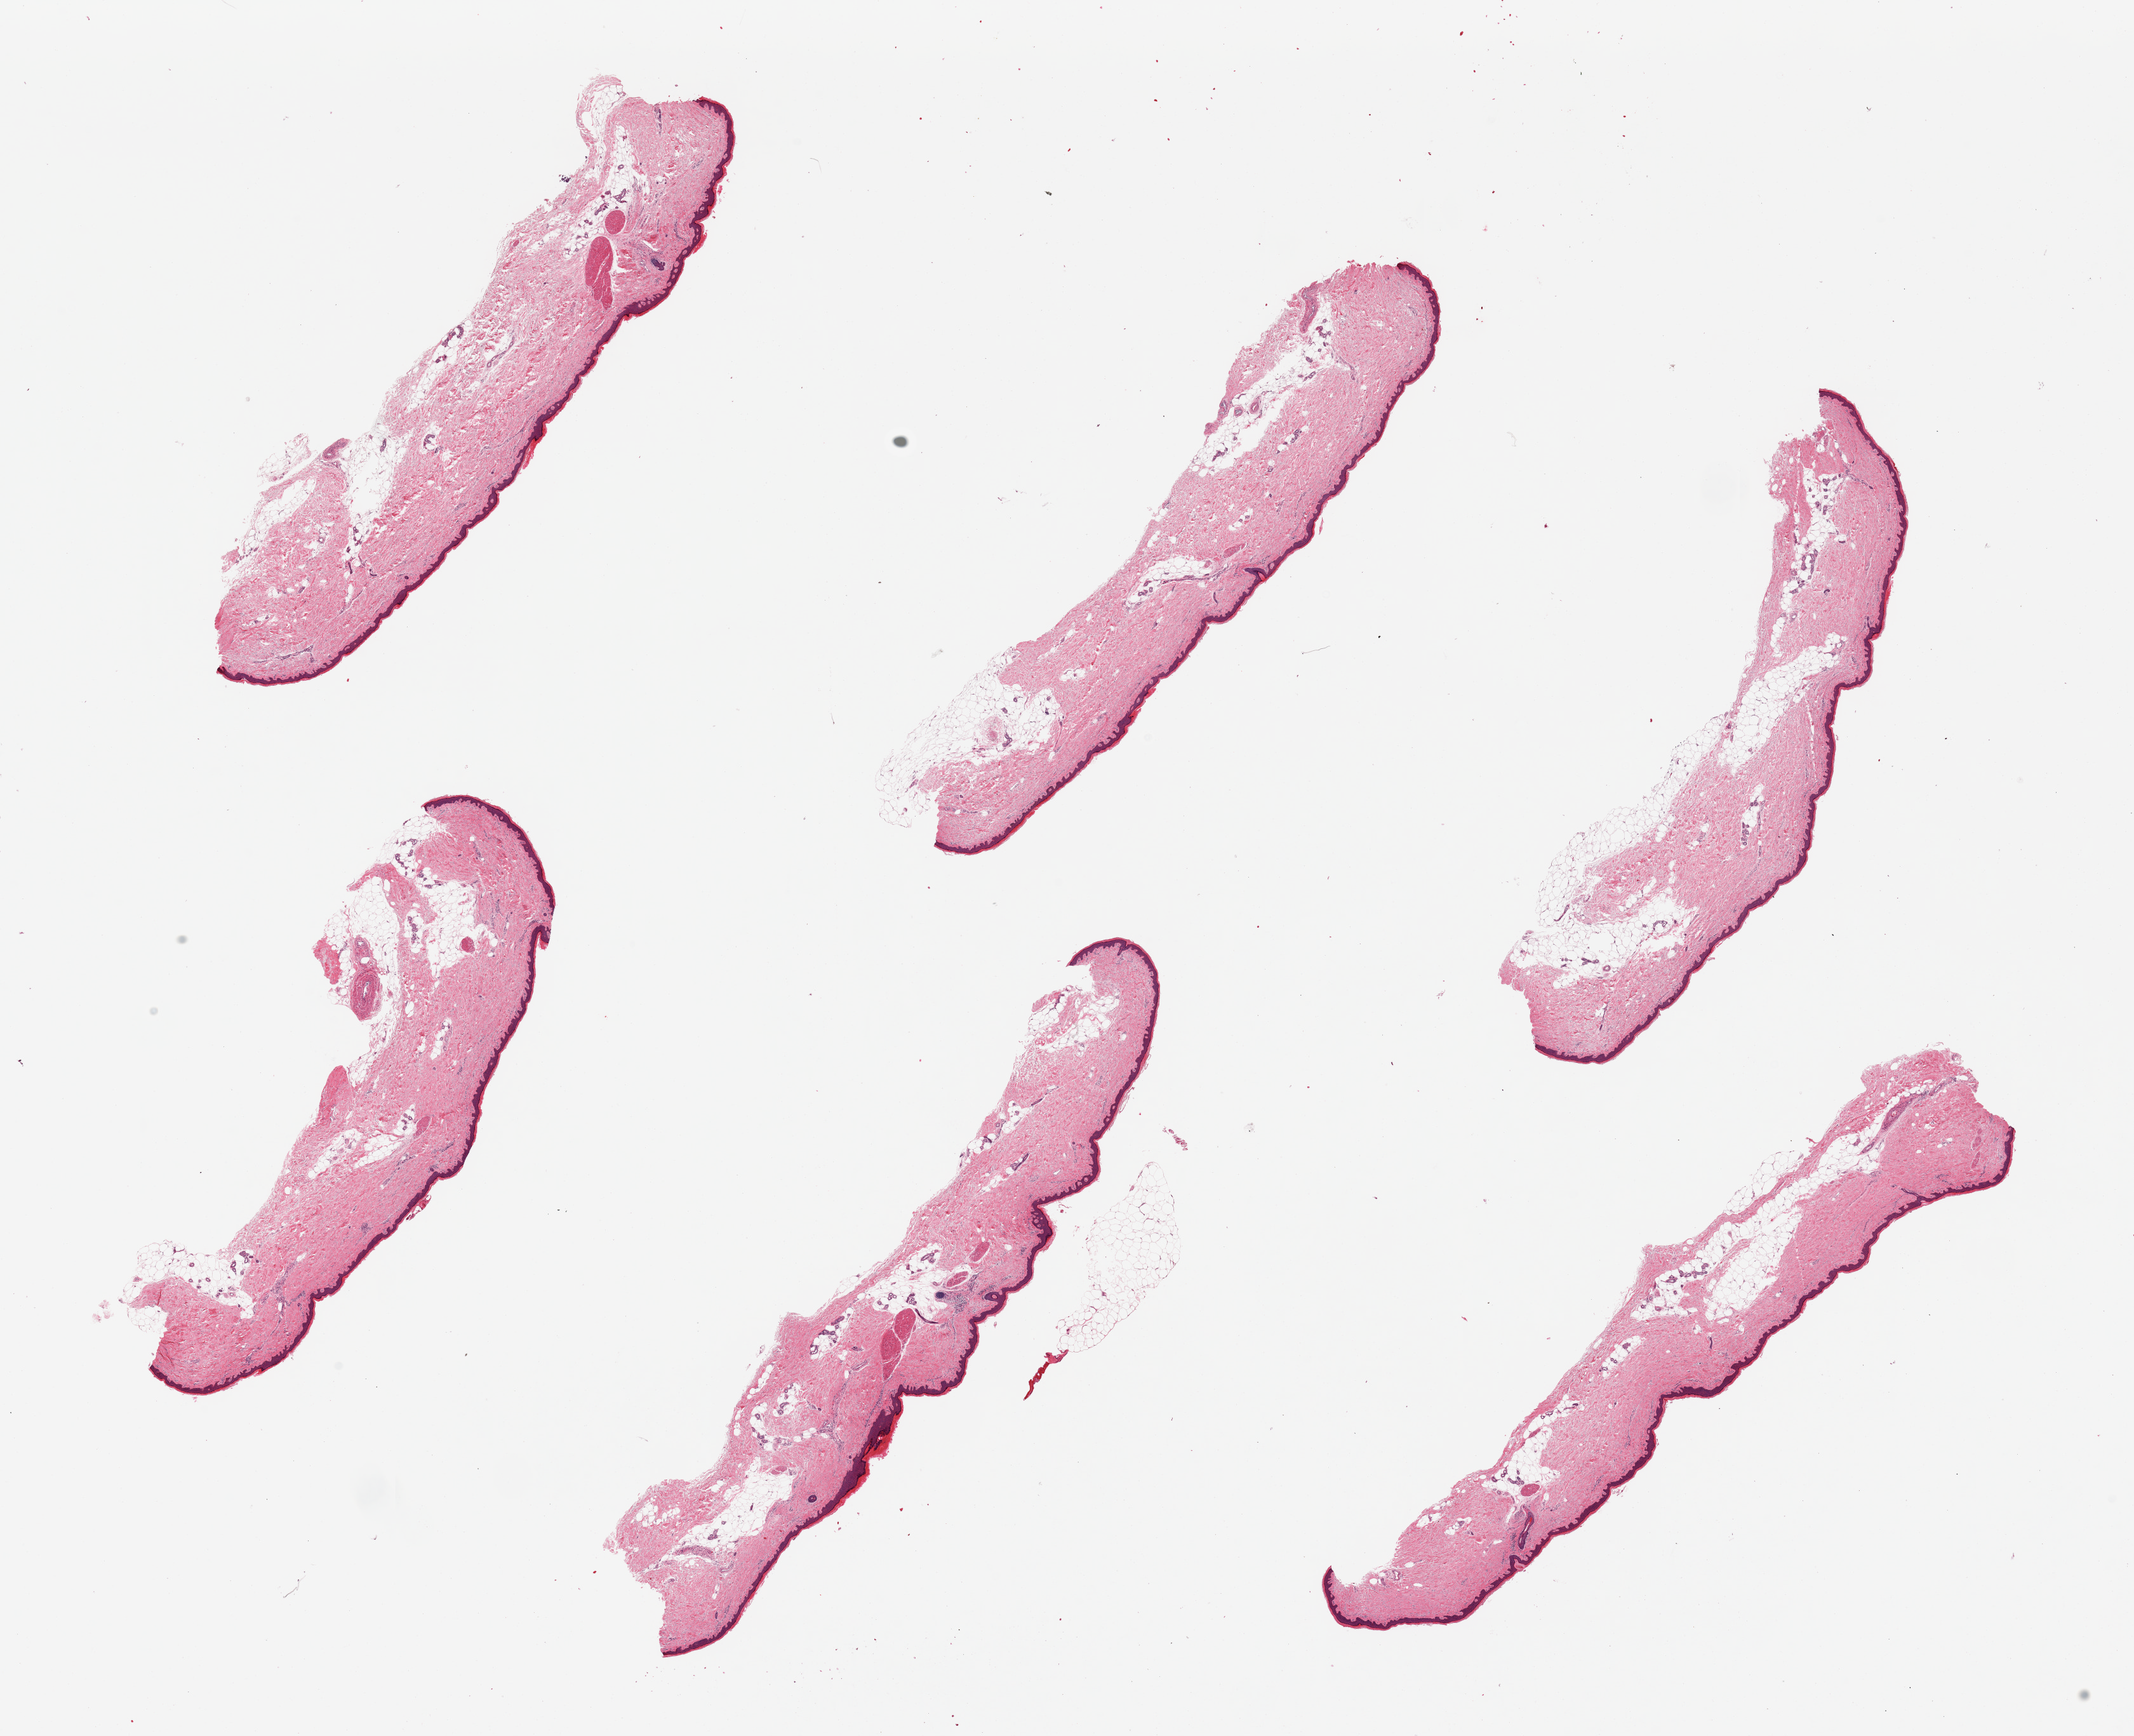
H&E whole-slide image, brightfield, a low-resolution overview of the entire scanned area, about 26.6 x 21.6 mm, PAXgene-fixed paraffin-embedded (PFPE) section, sampled site (target tissue): skin of lower leg, tissue donor sample. Donor sex: female.
* review note (as recorded): 6 pieces, internal and attached dermal adipose tissue of 5-15% in all pieces